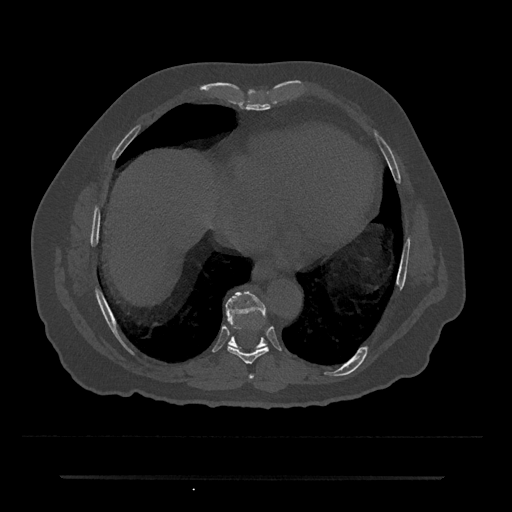
CT including the spine, one axial slice; position 313 of 797 along the scan axis; reconstruction kernel Br40s/3; 120 kVp; bone window (W 1800 / L 400 HU); 512 × 512 image matrix, field of view 437 × 437 mm. Patient: male, 69 years. From the clinical record (not read from this slice): primary cancer: prostate.
Outlined on this slice (semi-automatically segmented with operator editing):
- T7 vertebra: box from (x=249, y=375) to (x=254, y=379) px
- T8 vertebra: (x=227, y=328)–(x=269, y=364)
- T9 vertebra: (x=225, y=291)–(x=267, y=346)